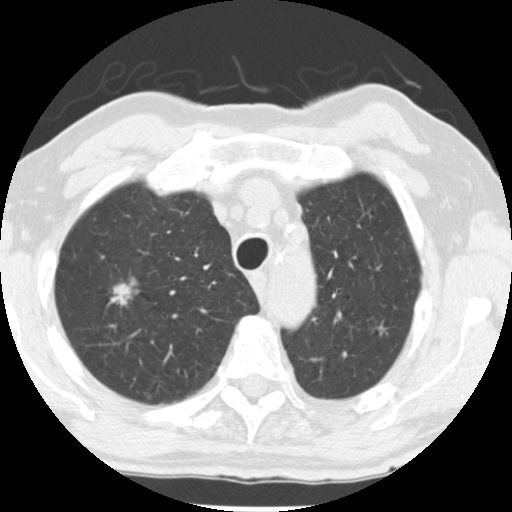
Low-dose screening chest CT, one axial slice. Position 201 of 252 along the scan axis. Reconstruction kernel STANDARD. 120 kVp. Lung window (W 1500 / L -600 HU). 512 × 512 image matrix, field of view 313 × 313 mm.
Structures marked on this image (manually delineated by an expert):
- lesion 1 (tumor, upper lobe of right lung): bounding box [x1, y1, x2, y2] px = [109, 279, 139, 306]